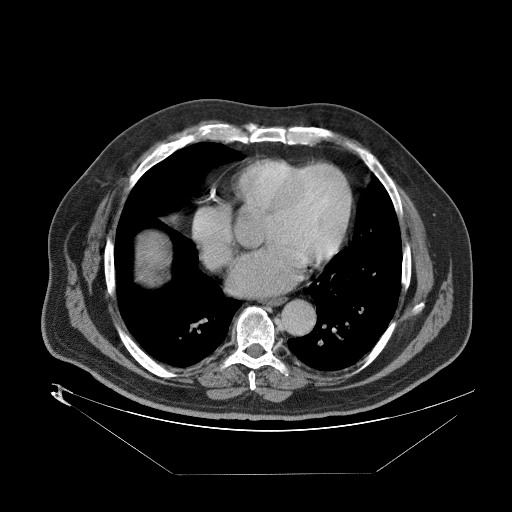
Contrast-enhanced abdominal CT (liver protocol), one axial slice. Slice 86 of 89 in the series (ordered by position). Reconstruction kernel STANDARD. 140 kVp. One of 2 acquisitions stored at this slice position. Soft-tissue window (W 400 / L 40 HU). 2.5 mm slice thickness. 512 × 512 image matrix. Case-level facts recorded for this patient, not image findings: diagnosis: hepatocellular carcinoma (patient treated with transarterial chemoembolisation; whether this scan precedes or follows treatment is not stated here); TNM stage (as recorded): Stage-II; Child-Pugh class: B; tumour differentiation: moderately differentiated; tumour nodularity: multinodular.
Structures marked on this image (semi-automatic segmentation, software-assisted and operator-edited):
- abdominal aorta: bounding box <279,300,313,335> (left, top, right, bottom; pixels)